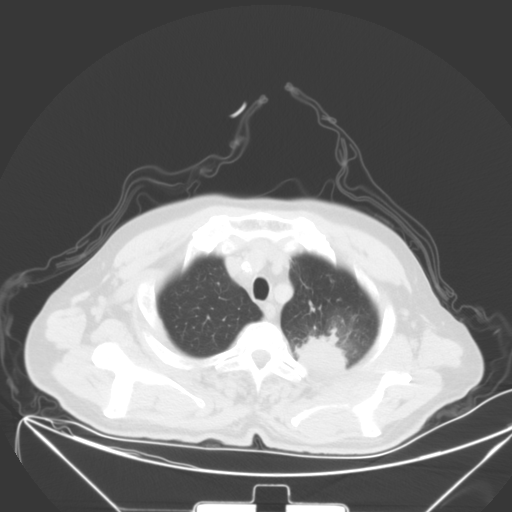
Chest CT, one axial slice. Slice 51 of 64 in the series (ordered by position). Lung window (W 1500 / L -600 HU). 5 mm slice thickness. 512 × 512 image matrix, field of view 431 × 431 mm. Patient: male, 58 years. From the clinical record (not read from this slice): clinical TNM (as recorded): T2b N3 M1b; histopathological grade: G3.
Outlined on this slice (bounding box drawn by a radiologist):
- lung tumour (recorded histology: adenocarcinoma): box from (x=296, y=331) to (x=351, y=382) px